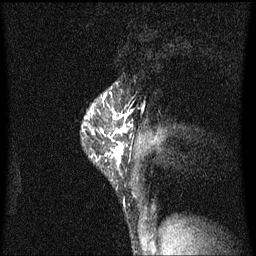
Breast MRI (dynamic contrast-enhanced), one sagittal slice. Slice 49 of 60 in the series (ordered by position). Dynamic contrast-enhanced series, image 2 of 3 at this slice position (ordered by acquisition). 1.5 T. TE 4.2 ms, TR 8.4 ms. 256 × 256 image matrix, field of view 200 × 200 mm. Patient: female, 40 years.
Annotated regions visible in this slice (semi-automatic segmentation, software-assisted and operator-edited):
- analysis volume of interest (the breast-tissue region the enhancement analysis was run in; not a lesion): box from (x=86, y=86) to (x=139, y=173) px
- tumour enhancement mask (voxels above the 70 % enhancement threshold inside the analysis volume of interest): (x=92, y=92)–(x=128, y=167)